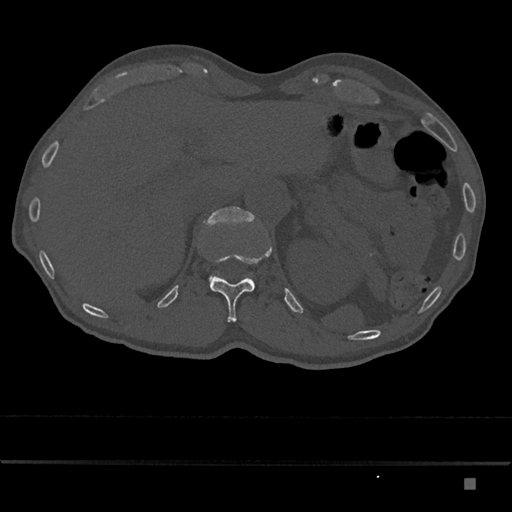
CT including the spine, one axial slice; slice 595 of 797 in the series (ordered by position); bone window (W 1800 / L 400 HU); 0.5 mm slice thickness; 512 × 512 image matrix, field of view 390 × 390 mm. Male patient, age 72 years. Case-level facts recorded for this patient, not image findings: primary cancer: prostate.
Outlined on this slice (semi-automatic segmentation, software-assisted and operator-edited):
- L1 vertebra: bounding box [x1, y1, x2, y2] px = [203, 207, 255, 288]
- T12 vertebra: [210, 247, 272, 322]